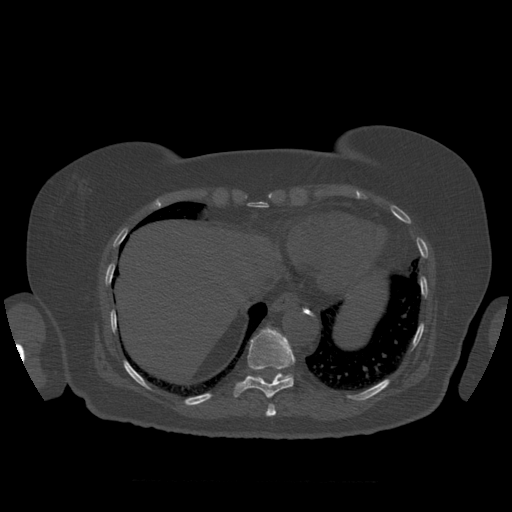
CT including the spine, one axial slice; slice 339 of 399 in the series (ordered by position); reconstruction kernel STANDARD; 120 kVp; bone window (W 1800 / L 400 HU); 512 × 512 image matrix, field of view 404 × 404 mm. Patient age 81 years. From the clinical record (not read from this slice): primary cancer: renal; vertebrae with lytic lesions (as recorded): L1.
Outlined on this slice (semi-automatically segmented with operator editing):
- T10 vertebra: box from (x=234, y=328) to (x=296, y=399) px
- T11 vertebra: (x=283, y=374)–(x=291, y=379)
- T9 vertebra: (x=266, y=404)–(x=276, y=417)